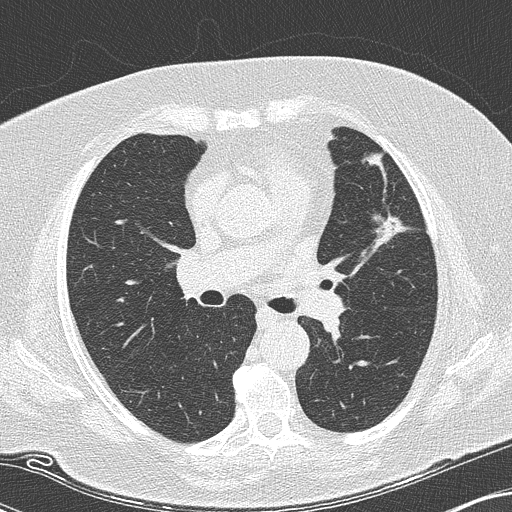
Chest CT (low-dose screening protocol), one axial image; second annual screen; lung window (W 1500 / L -600 HU); 2 mm slice thickness; slice 57 of 151 in the series. Female, age 73 years at enrolment. Current smoker at enrolment.
• Lesion marked by an expert reader, bounding box [x1, y1, x2, y2] px = [364, 208, 404, 250].
• The screening reader recorded 2 non-calcified nodules or masses ≥4 mm on this exam (lingula, right lower lobe); which of them this box marks is not recorded.
• Participant outcome: lung cancer diagnosed 123 days after this screen — adenocarcinoma, NOS, left upper lobe, moderately differentiated (G2), stage IIIB (AJCC 6th edition), 12 mm at pathology.